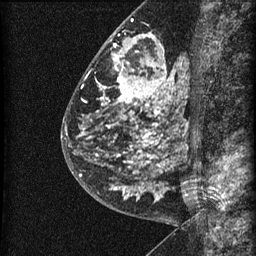
Breast MRI (dynamic contrast-enhanced), one sagittal slice. Position 27 of 60 along the scan axis. Dynamic contrast-enhanced series, image 2 of 3 at this slice position (ordered by acquisition). 1.5 T. TE 4.2 ms, TR 22.7 ms. 1.5 mm slice thickness. 256 × 256 image matrix. Patient: female, 48 years. Case-level facts recorded for this patient, not image findings: setting: breast cancer imaged before/during neoadjuvant chemotherapy; receptor status: triple-negative.
Structures marked on this image (semi-automatic segmentation, software-assisted and operator-edited):
- analysis volume of interest (the breast-tissue region the enhancement analysis was run in; not a lesion): bounding box [x1, y1, x2, y2] px = [81, 23, 186, 202]
- tumour enhancement mask (voxels above the 90 % enhancement threshold inside the analysis volume of interest): [96, 34, 181, 198]